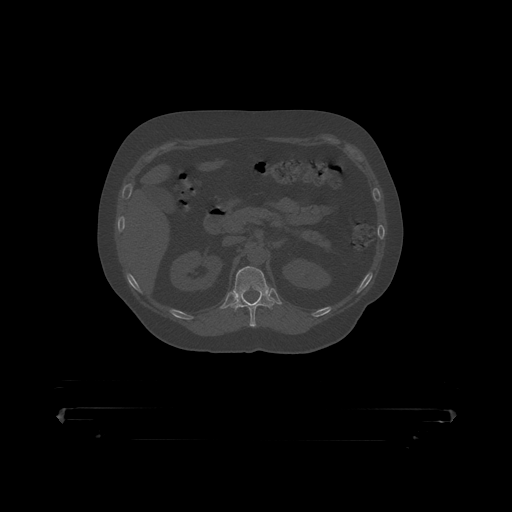
CT including the spine, one axial slice; position 172 of 390 along the scan axis; reconstruction kernel STANDARD; bone window (W 1800 / L 400 HU); 1.25 mm slice thickness; 512 × 512 image matrix, field of view 650 × 650 mm. Male patient, age 60 years. Case-level facts recorded for this patient, not image findings: primary cancer: prostate.
Structures marked on this image (semi-automatic segmentation, software-assisted and operator-edited):
- T12 vertebra: bounding box <230,267,275,319> (left, top, right, bottom; pixels)